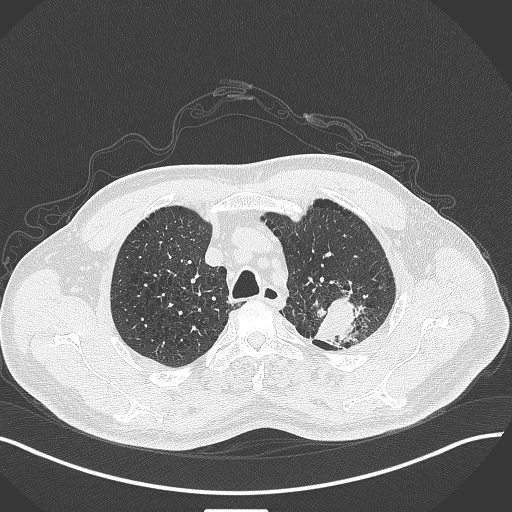
Chest CT, one axial slice; position 343 of 429 along the scan axis; reconstruction kernel B70f; 120 kVp; lung window (W 1500 / L -600 HU); 1 mm slice thickness; 512 × 512 image matrix, field of view 400 × 400 mm. Patient: male, 55 years. Case-level facts recorded for this patient, not image findings: clinical TNM (as recorded): T3 N0 M1c; histopathological grade: G3.
Outlined on this slice (rectangle marked by the reading radiologist):
- lung tumour (recorded histology: adenocarcinoma): bounding box <309,291,369,354> (left, top, right, bottom; pixels)